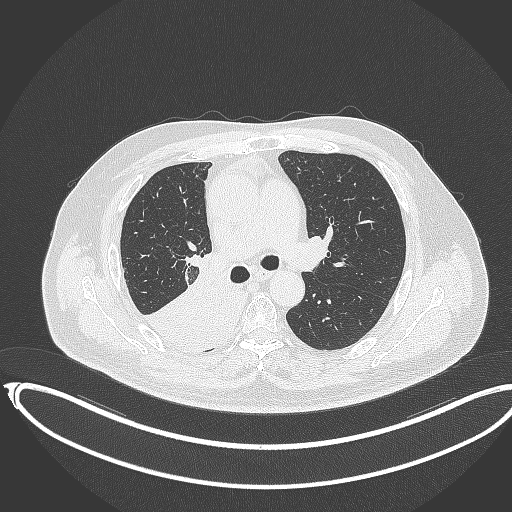
Chest CT, one axial slice; slice 221 of 403 in the series (ordered by position); 120 kVp; lung window (W 1500 / L -600 HU); 512 × 512 image matrix, field of view 436 × 436 mm. Patient: male, 68 years. From the clinical record (not read from this slice): clinical TNM (as recorded): T2a N0 M0.
Structures marked on this image (bounding box drawn by a radiologist):
- lung tumour (recorded histology: adenocarcinoma): bounding box [x1, y1, x2, y2] px = [146, 267, 248, 356]